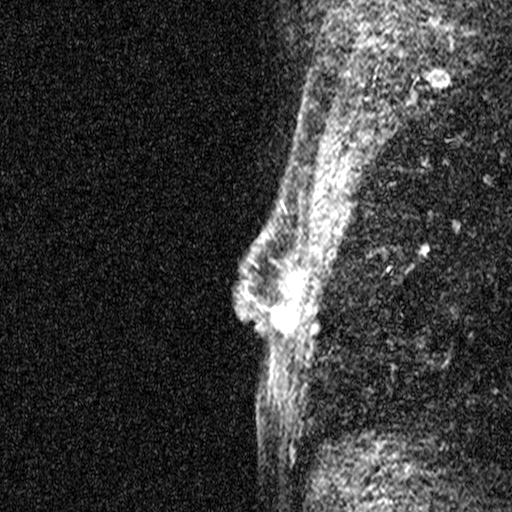
Breast MRI (dynamic contrast-enhanced), one sagittal slice. Position 29 of 44 along the scan axis. Dynamic contrast-enhanced study with each time point stored as its own series, time point 2 of 3 at this slice position (early post-contrast, ordered by acquisition time). 1.5 T. TE 4.5 ms, TR 11 ms. 512 × 512 image matrix, field of view 200 × 200 mm. Patient: female, 45 years. Case-level facts recorded for this patient, not image findings: setting: breast cancer imaged before/during neoadjuvant chemotherapy; receptor status: HR-positive, HER2-negative.
Annotated regions visible in this slice (semi-automatically segmented with operator editing):
- analysis volume of interest (the breast-tissue region the enhancement analysis was run in; not a lesion): bounding box <256,218,308,359> (left, top, right, bottom; pixels)
- tumour enhancement mask (voxels above the 90 % enhancement threshold inside the analysis volume of interest): <257,267,296,331>